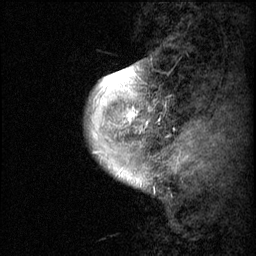
Breast MRI (dynamic contrast-enhanced), one sagittal slice; position 6 of 60 along the scan axis; dynamic contrast-enhanced series, image 2 of 3 at this slice position (ordered by acquisition); 1.5 T; TE 4.2 ms, TR 11.1 ms; 2 mm slice thickness; 256 × 256 image matrix, field of view 180 × 180 mm. Patient: female, 50 years.
Annotated regions visible in this slice (semi-automatically segmented with operator editing):
- analysis volume of interest (the breast-tissue region the enhancement analysis was run in; not a lesion): bounding box [x1, y1, x2, y2] px = [85, 60, 157, 143]
- tumour enhancement mask (voxels above the 70 % enhancement threshold inside the analysis volume of interest): [99, 62, 142, 143]